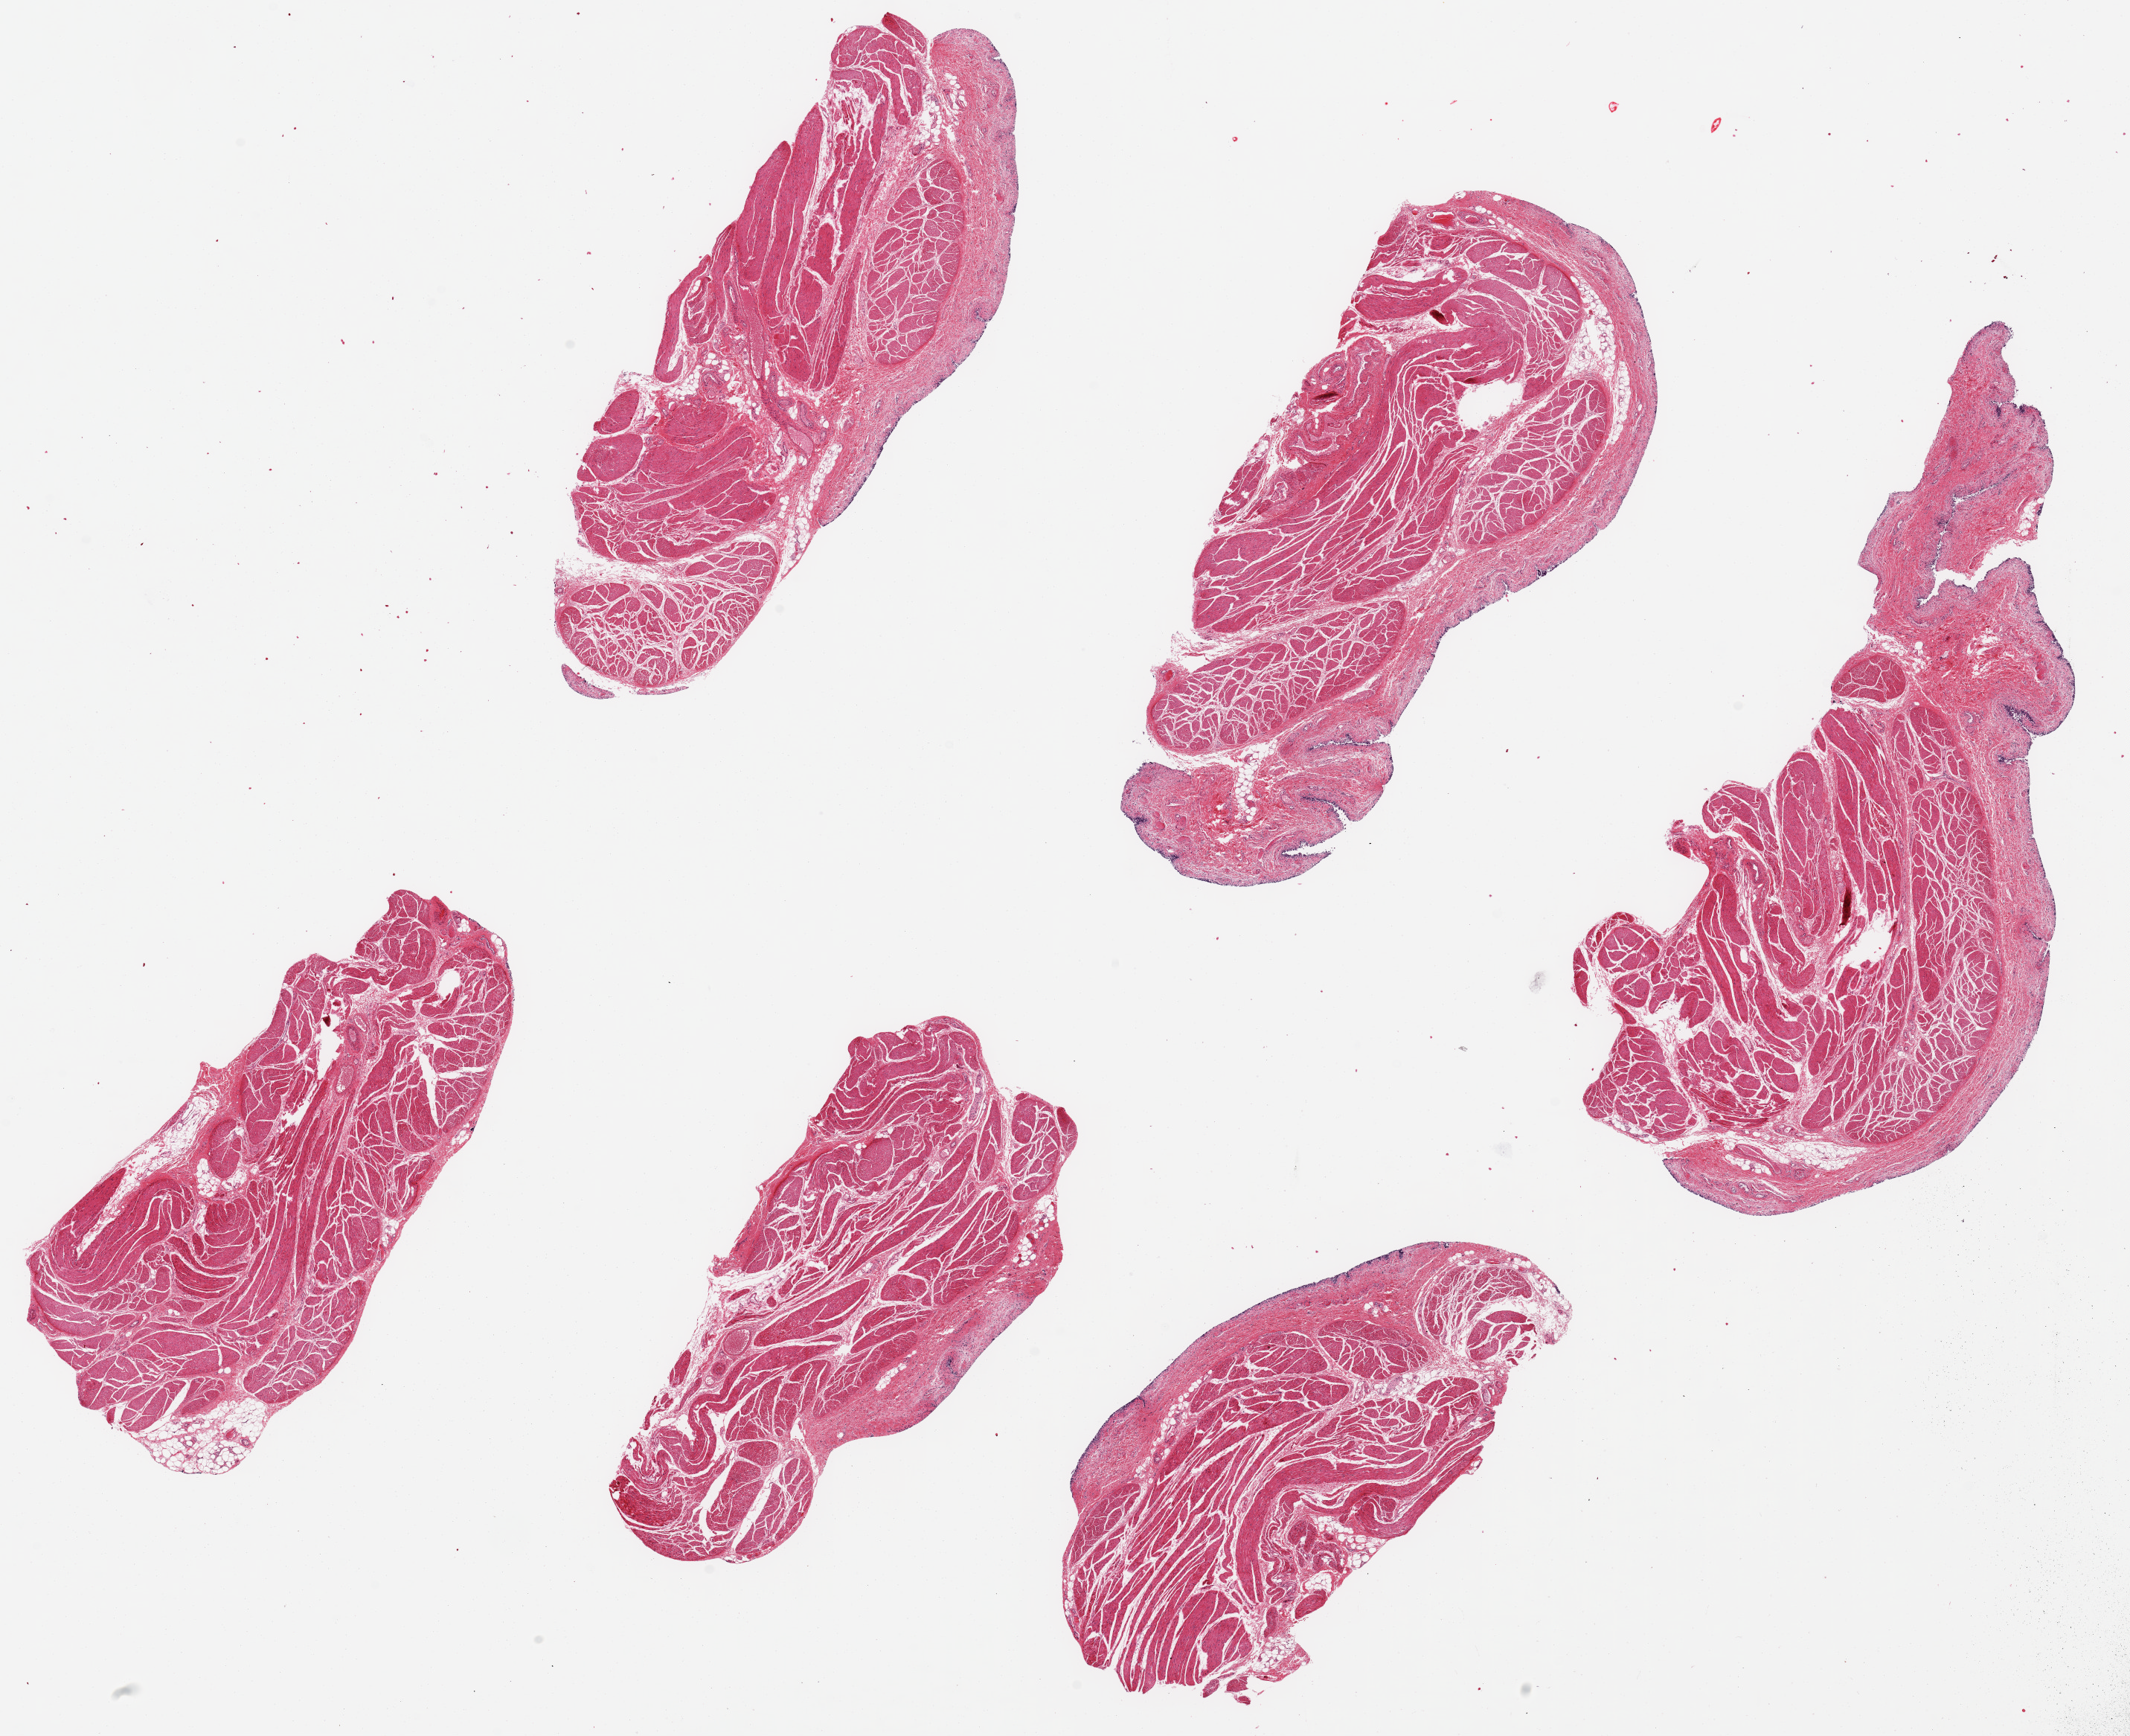
Whole-slide image, hematoxylin and eosin (H&E) stain, brightfield — low-resolution overview of the scanned area, about 22.6 x 18.5 mm (acquisition: 20x scan), PAXgene-fixed paraffin-embedded (PFPE) section, target tissue: urinary bladder, donor tissue sample. Donor: male.
Reviewer comment on this tissue sample: 6 ~7.5x3.5mm pieces. Urothelium essentially completely sloughed, or focally 1-2 badly autolyzed cell layers remain.